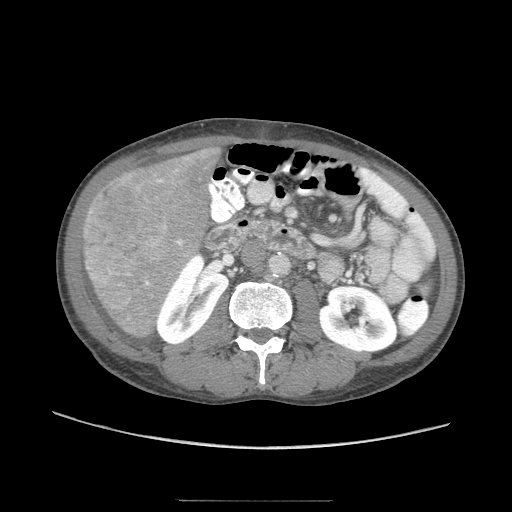
Contrast-enhanced abdominal CT (liver protocol), one axial slice. Slice 19 of 103 in the series (ordered by position). Soft-tissue window (W 400 / L 40 HU). 2.5 mm slice thickness. 512 × 512 image matrix, field of view 380 × 380 mm. Case-level facts recorded for this patient, not image findings: diagnosis: hepatocellular carcinoma (patient treated with transarterial chemoembolisation; whether this scan precedes or follows treatment is not stated here); TNM stage (as recorded): Stage-IIIA.
Outlined on this slice (semi-automatic segmentation, software-assisted and operator-edited):
- liver parenchyma outside the tumour (the mass and vessels are separate outlines, so this box may not span the whole liver): bounding box [x1, y1, x2, y2] px = [82, 146, 221, 334]
- mass: [81, 167, 179, 311]